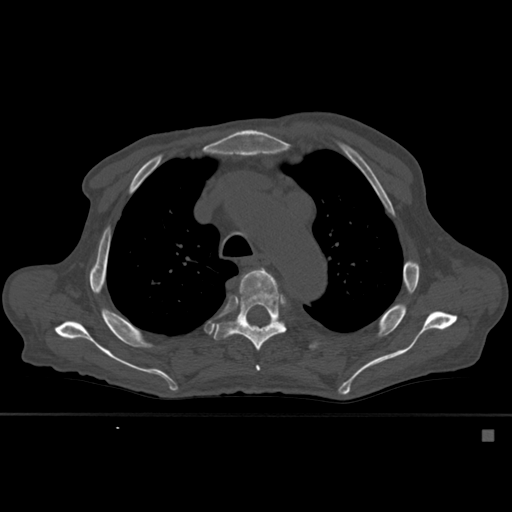
CT including the spine, one axial slice. Position 403 of 527 along the scan axis. Bone window (W 1800 / L 400 HU). 1.5 mm slice thickness. 512 × 512 image matrix. Male patient, age 78 years. From the clinical record (not read from this slice): primary cancer: prostate.
Annotated regions visible in this slice (semi-automatic segmentation, software-assisted and operator-edited):
- T4 vertebra: bounding box [x1, y1, x2, y2] px = [242, 268, 274, 371]
- T5 vertebra: [214, 268, 287, 351]